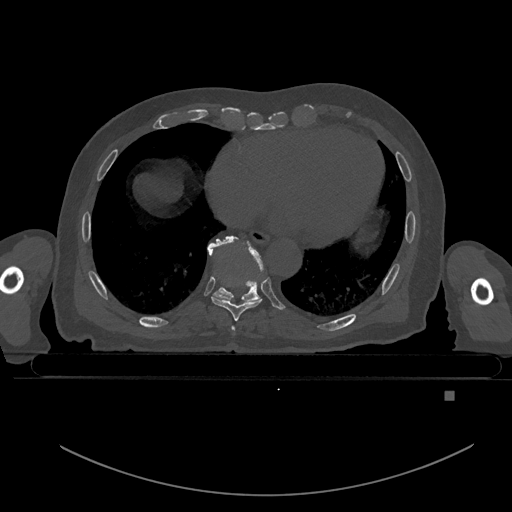
CT including the spine, one axial slice. Position 181 of 969 along the scan axis. Bone window (W 1800 / L 400 HU). 0.5 mm slice thickness. 512 × 512 image matrix, field of view 456 × 456 mm. Patient: male, 82 years. Case-level facts recorded for this patient, not image findings: primary cancer: prostate.
Structures marked on this image (semi-automatically segmented with operator editing):
- T7 vertebra: bounding box (x1, y1, x2, y2) in pixels: (232, 327, 235, 332)
- T8 vertebra: (211, 268, 262, 321)
- T9 vertebra: (207, 235, 263, 302)